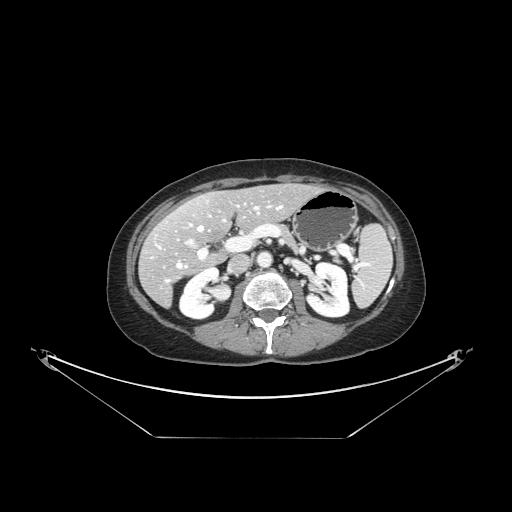
Contrast-enhanced abdominal CT, one axial slice; reconstruction kernel STANDARD; intravenous contrast given; soft-tissue window (W 400 / L 40 HU); 512 × 512 image matrix, field of view 500 × 500 mm. Female patient, age 73 years. From the clinical record (not read from this slice): diagnosis: colorectal cancer liver metastases, imaged before liver resection; multiple liver metastases: no.
Outlined on this slice (outlined manually by an expert reader):
- hepatic veins: bounding box [x1, y1, x2, y2] px = [157, 205, 283, 282]
- liver: [140, 185, 317, 306]
- planned liver remnant (the part of the liver to remain after resection): [168, 185, 317, 244]
- portal vein (with intrahepatic branches): [178, 206, 260, 260]